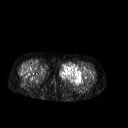
FDG PET of an extremity soft-tissue mass (from a PET/CT study), one axial slice. Slice 243 of 267 in the series (ordered by position). 3.27 mm slice thickness. 128 × 128 image matrix, field of view 500 × 500 mm. Female patient, age 42 years. From the clinical record (not read from this slice): histological type: pleiomorphic leiomyosarcoma; grade: intermediate; site of the primary tumour: left thigh.
Structures marked on this image (expert contour drawn on MRI and transferred to this co-registered scan by the dataset authors):
- gross tumour volume including surrounding oedema: box from (x=59, y=64) to (x=82, y=82) px
- gross tumour volume (mass): (x=59, y=64)–(x=82, y=82)